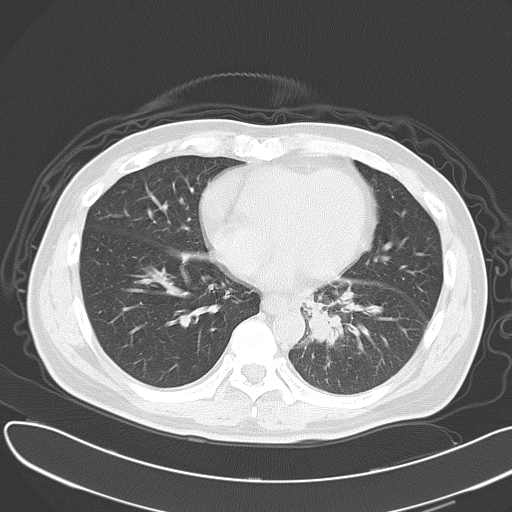
Chest CT, one axial slice. Reconstruction kernel B70f. Lung window (W 1500 / L -600 HU). 5 mm slice thickness. 512 × 512 image matrix, field of view 376 × 376 mm. Male patient, age 55 years. Case-level facts recorded for this patient, not image findings: clinical TNM (as recorded): T2 N3 M0.
Structures marked on this image (rectangle marked by the reading radiologist):
- lung tumour (recorded histology: small cell carcinoma): box from (x=301, y=301) to (x=344, y=359) px